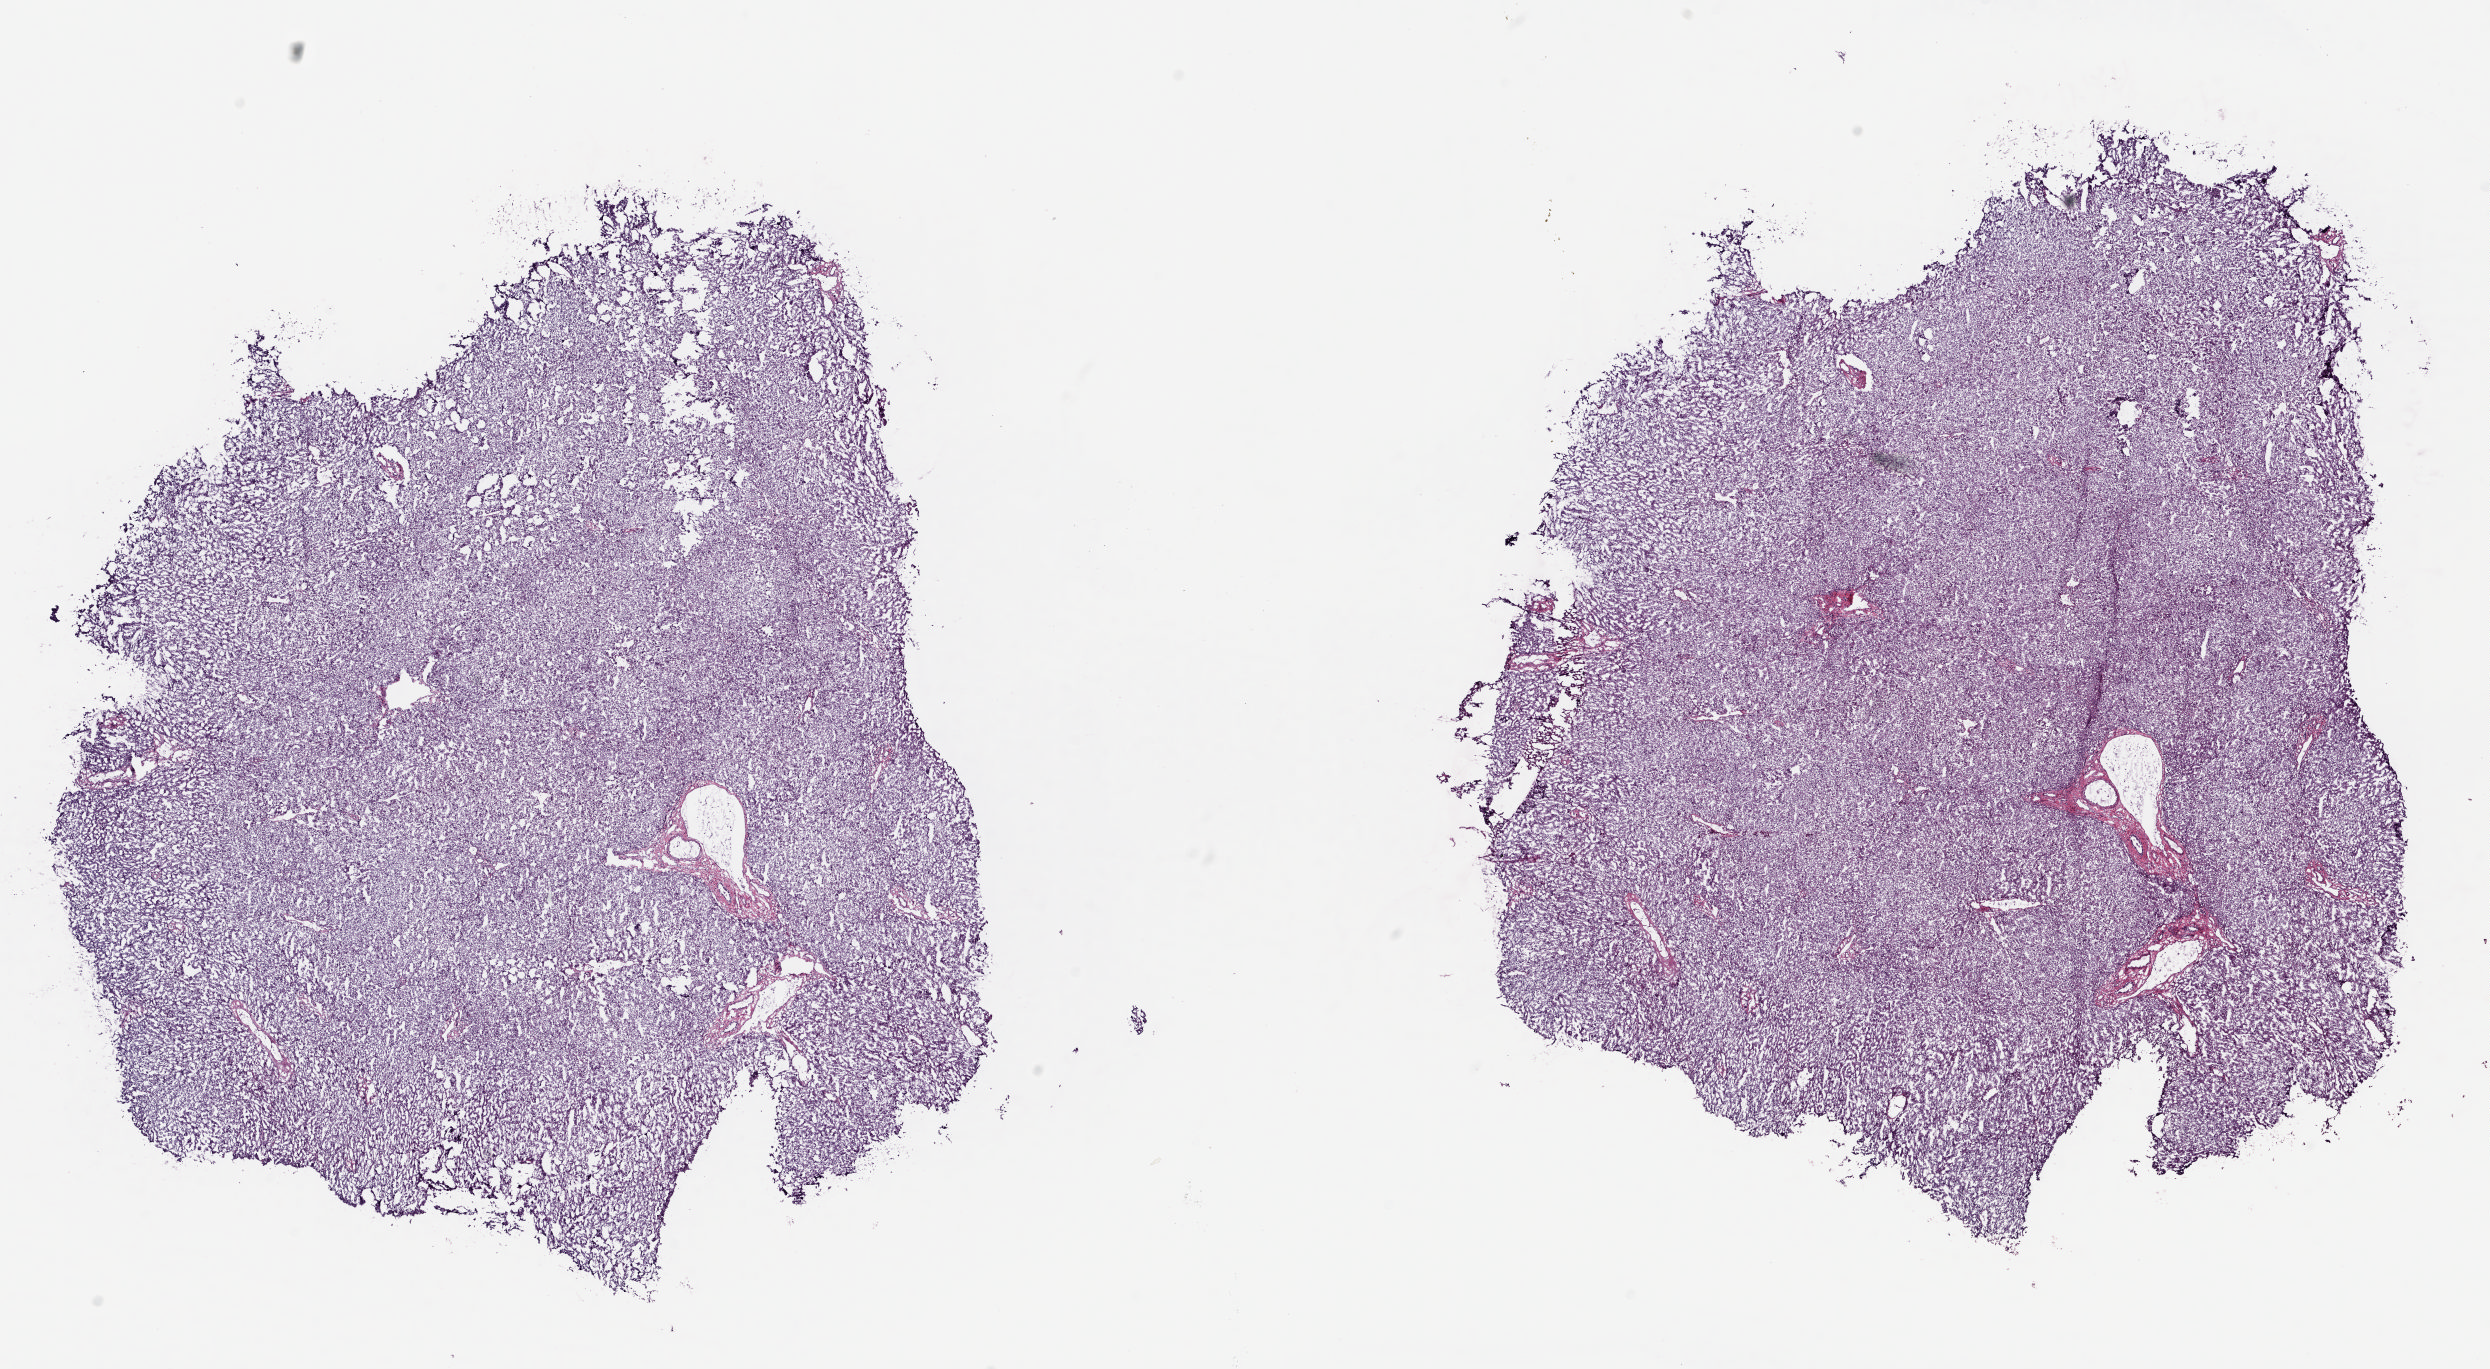
Digitized H&E tissue section (whole slide), a low-resolution overview of the entire scanned area, about 19.8 x 10.9 mm (acquisition: 20x scan); frozen section; solid tissue normal (non-tumour tissue) sample from the liver. Patient: female, age at initial diagnosis 52 years.
This section: solid tissue normal sample (biorepository sample class). Patient diagnosis: Hepatocellular carcinoma, NOS.